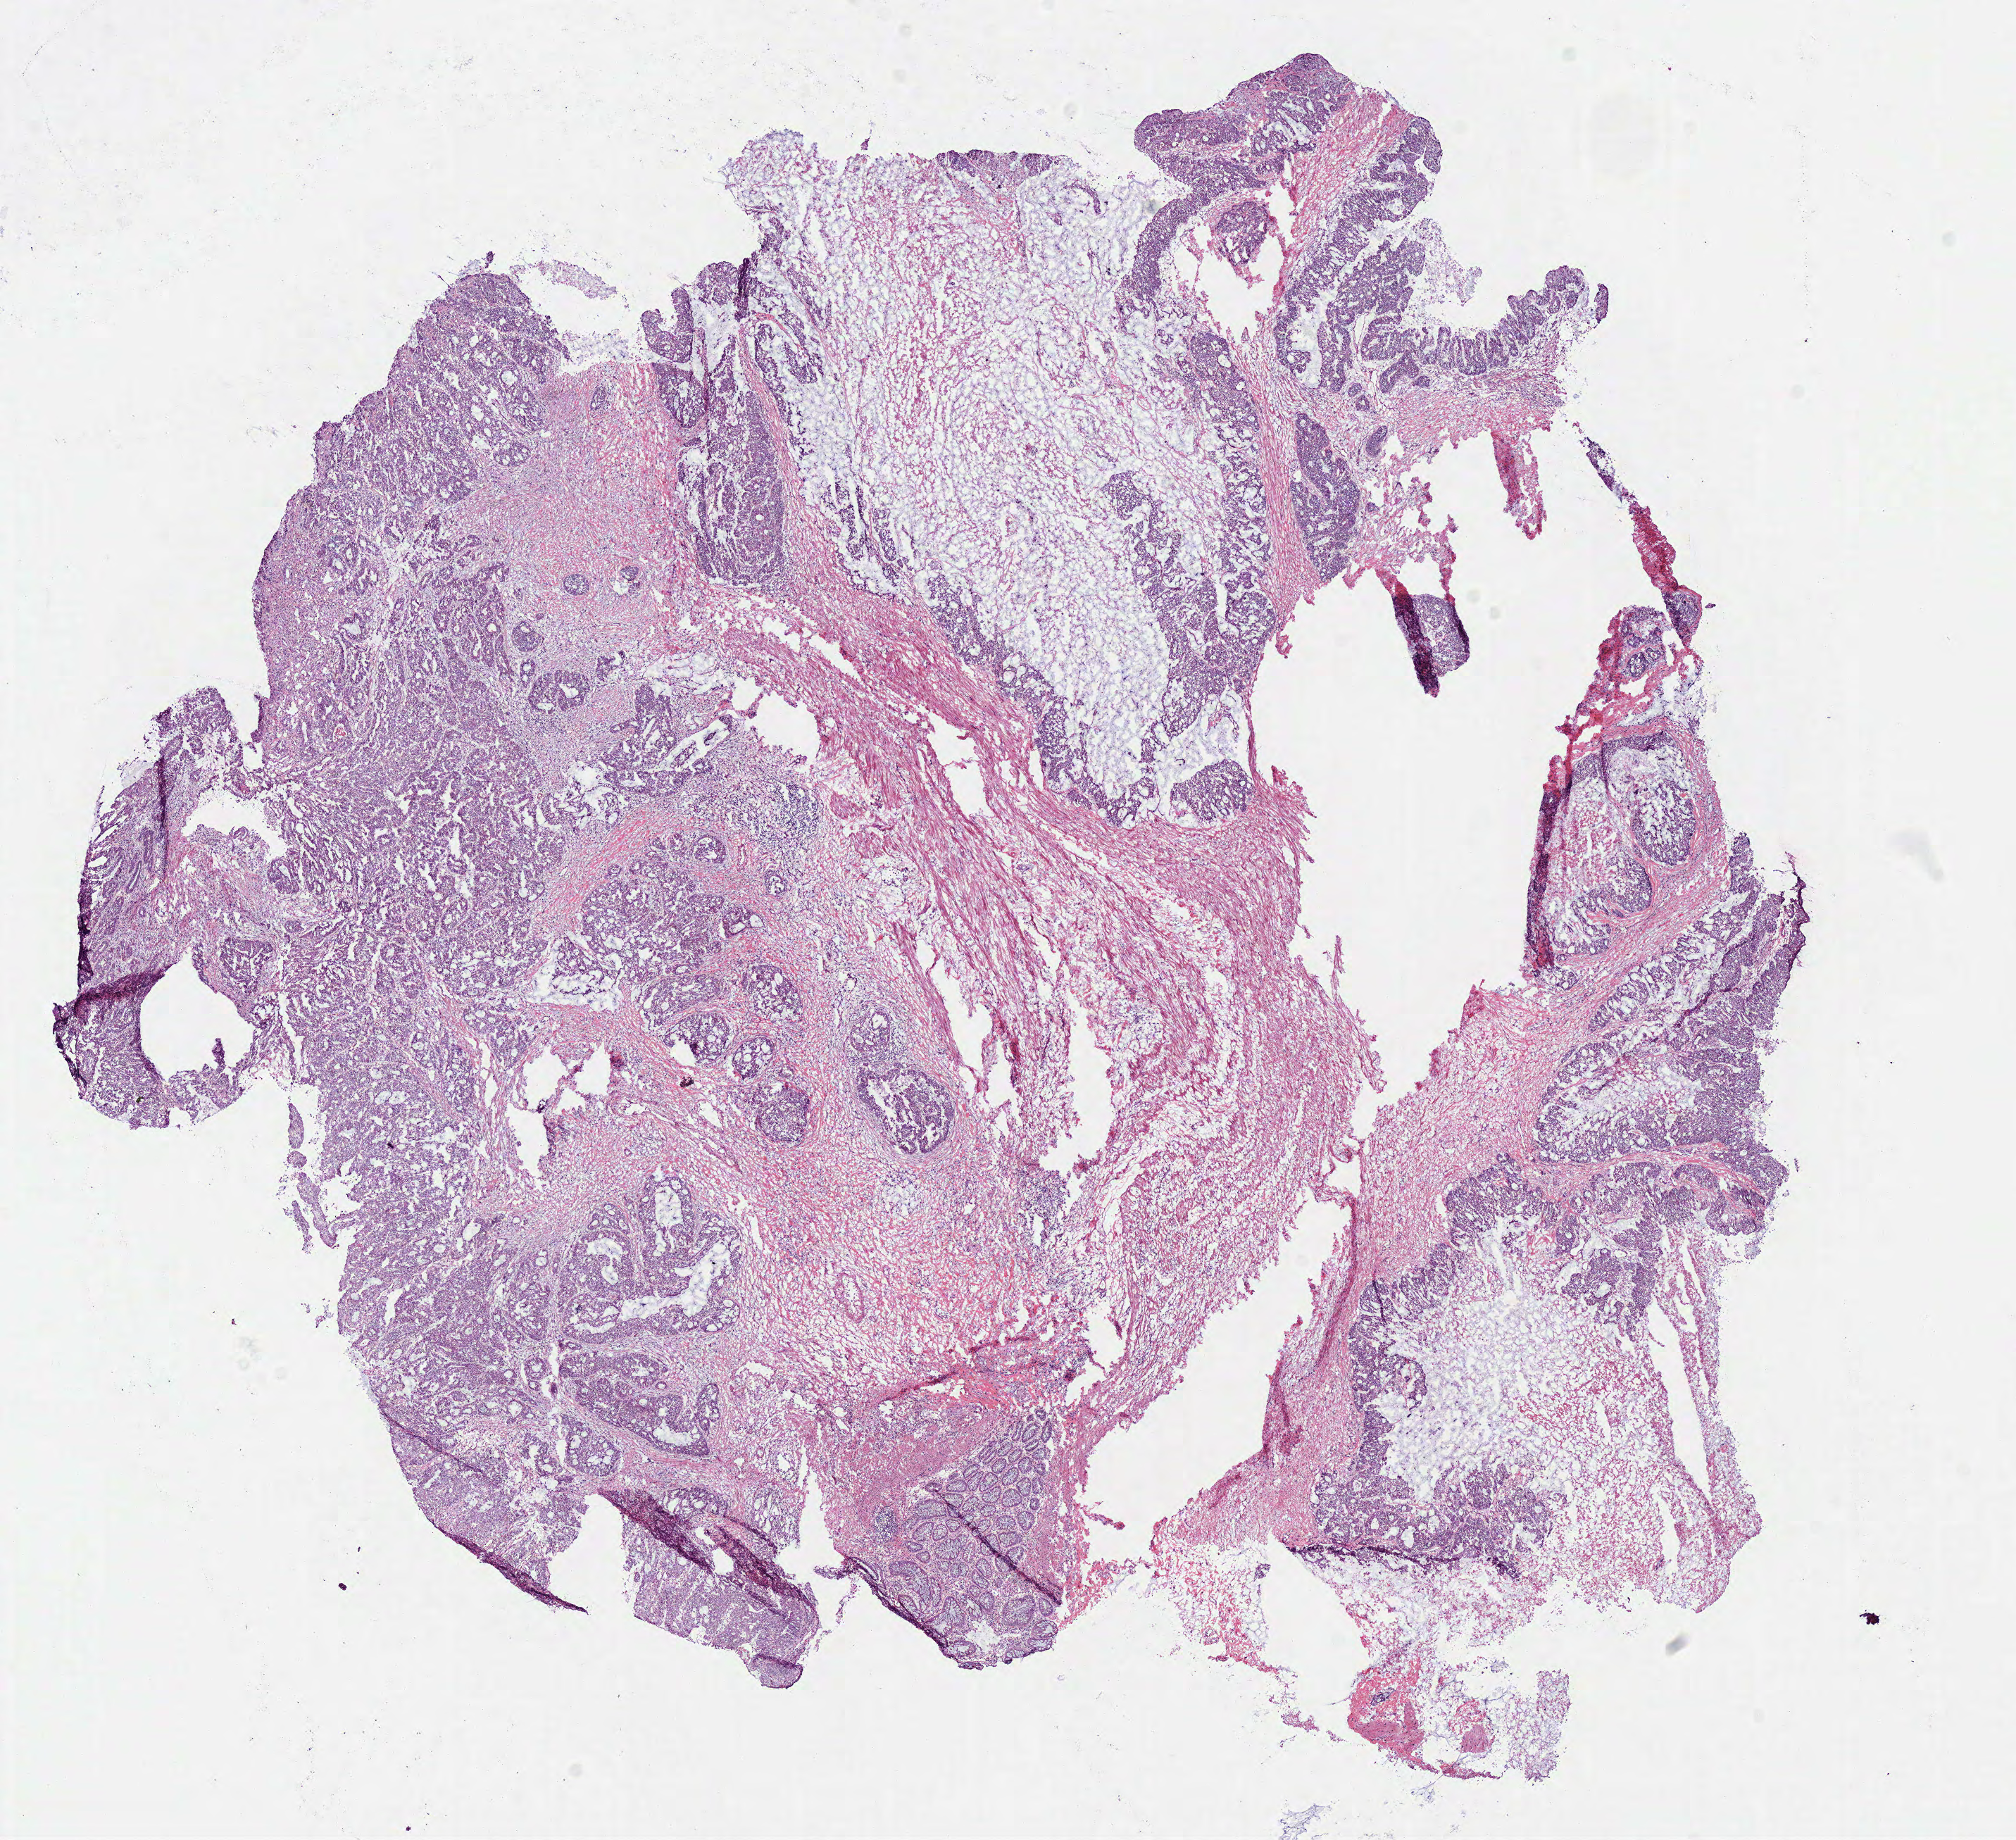
Digitized Hematoxylin and eosin (H&E) stained tissue section (whole slide), whole scanned area (about 11.3 x 10.3 mm) shown as a low-resolution overview, frozen section from the bottom of the tissue portion, primary tumour sample from the colon. Patient: male, age at initial diagnosis 74 years. Pathologist review of this section (percent, as recorded): tumour cells 70%, tumour nuclei 80%, normal cells 0%, stromal cells 20%, necrosis 10%.
- diagnosis: Adenocarcinoma, NOS (sigmoid colon)
- AJCC pathologic stage: IIA
- lymph nodes positive (case pathology): 0 of 20 examined